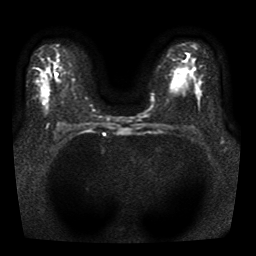
Breast MRI, one axial slice. Slice 27 of 41 in the series (ordered by position). Diffusion-weighted series; image 2 of 4 stored at this slice position (different b-values; order by instance number). 1.5 T. 5 mm slice thickness. 256 × 256 image matrix, field of view 330 × 330 mm. Female patient.
Annotated regions visible in this slice (expert manual segmentation):
- tumour on diffusion-weighted imaging: bounding box (x1, y1, x2, y2) in pixels: (40, 94, 48, 102)